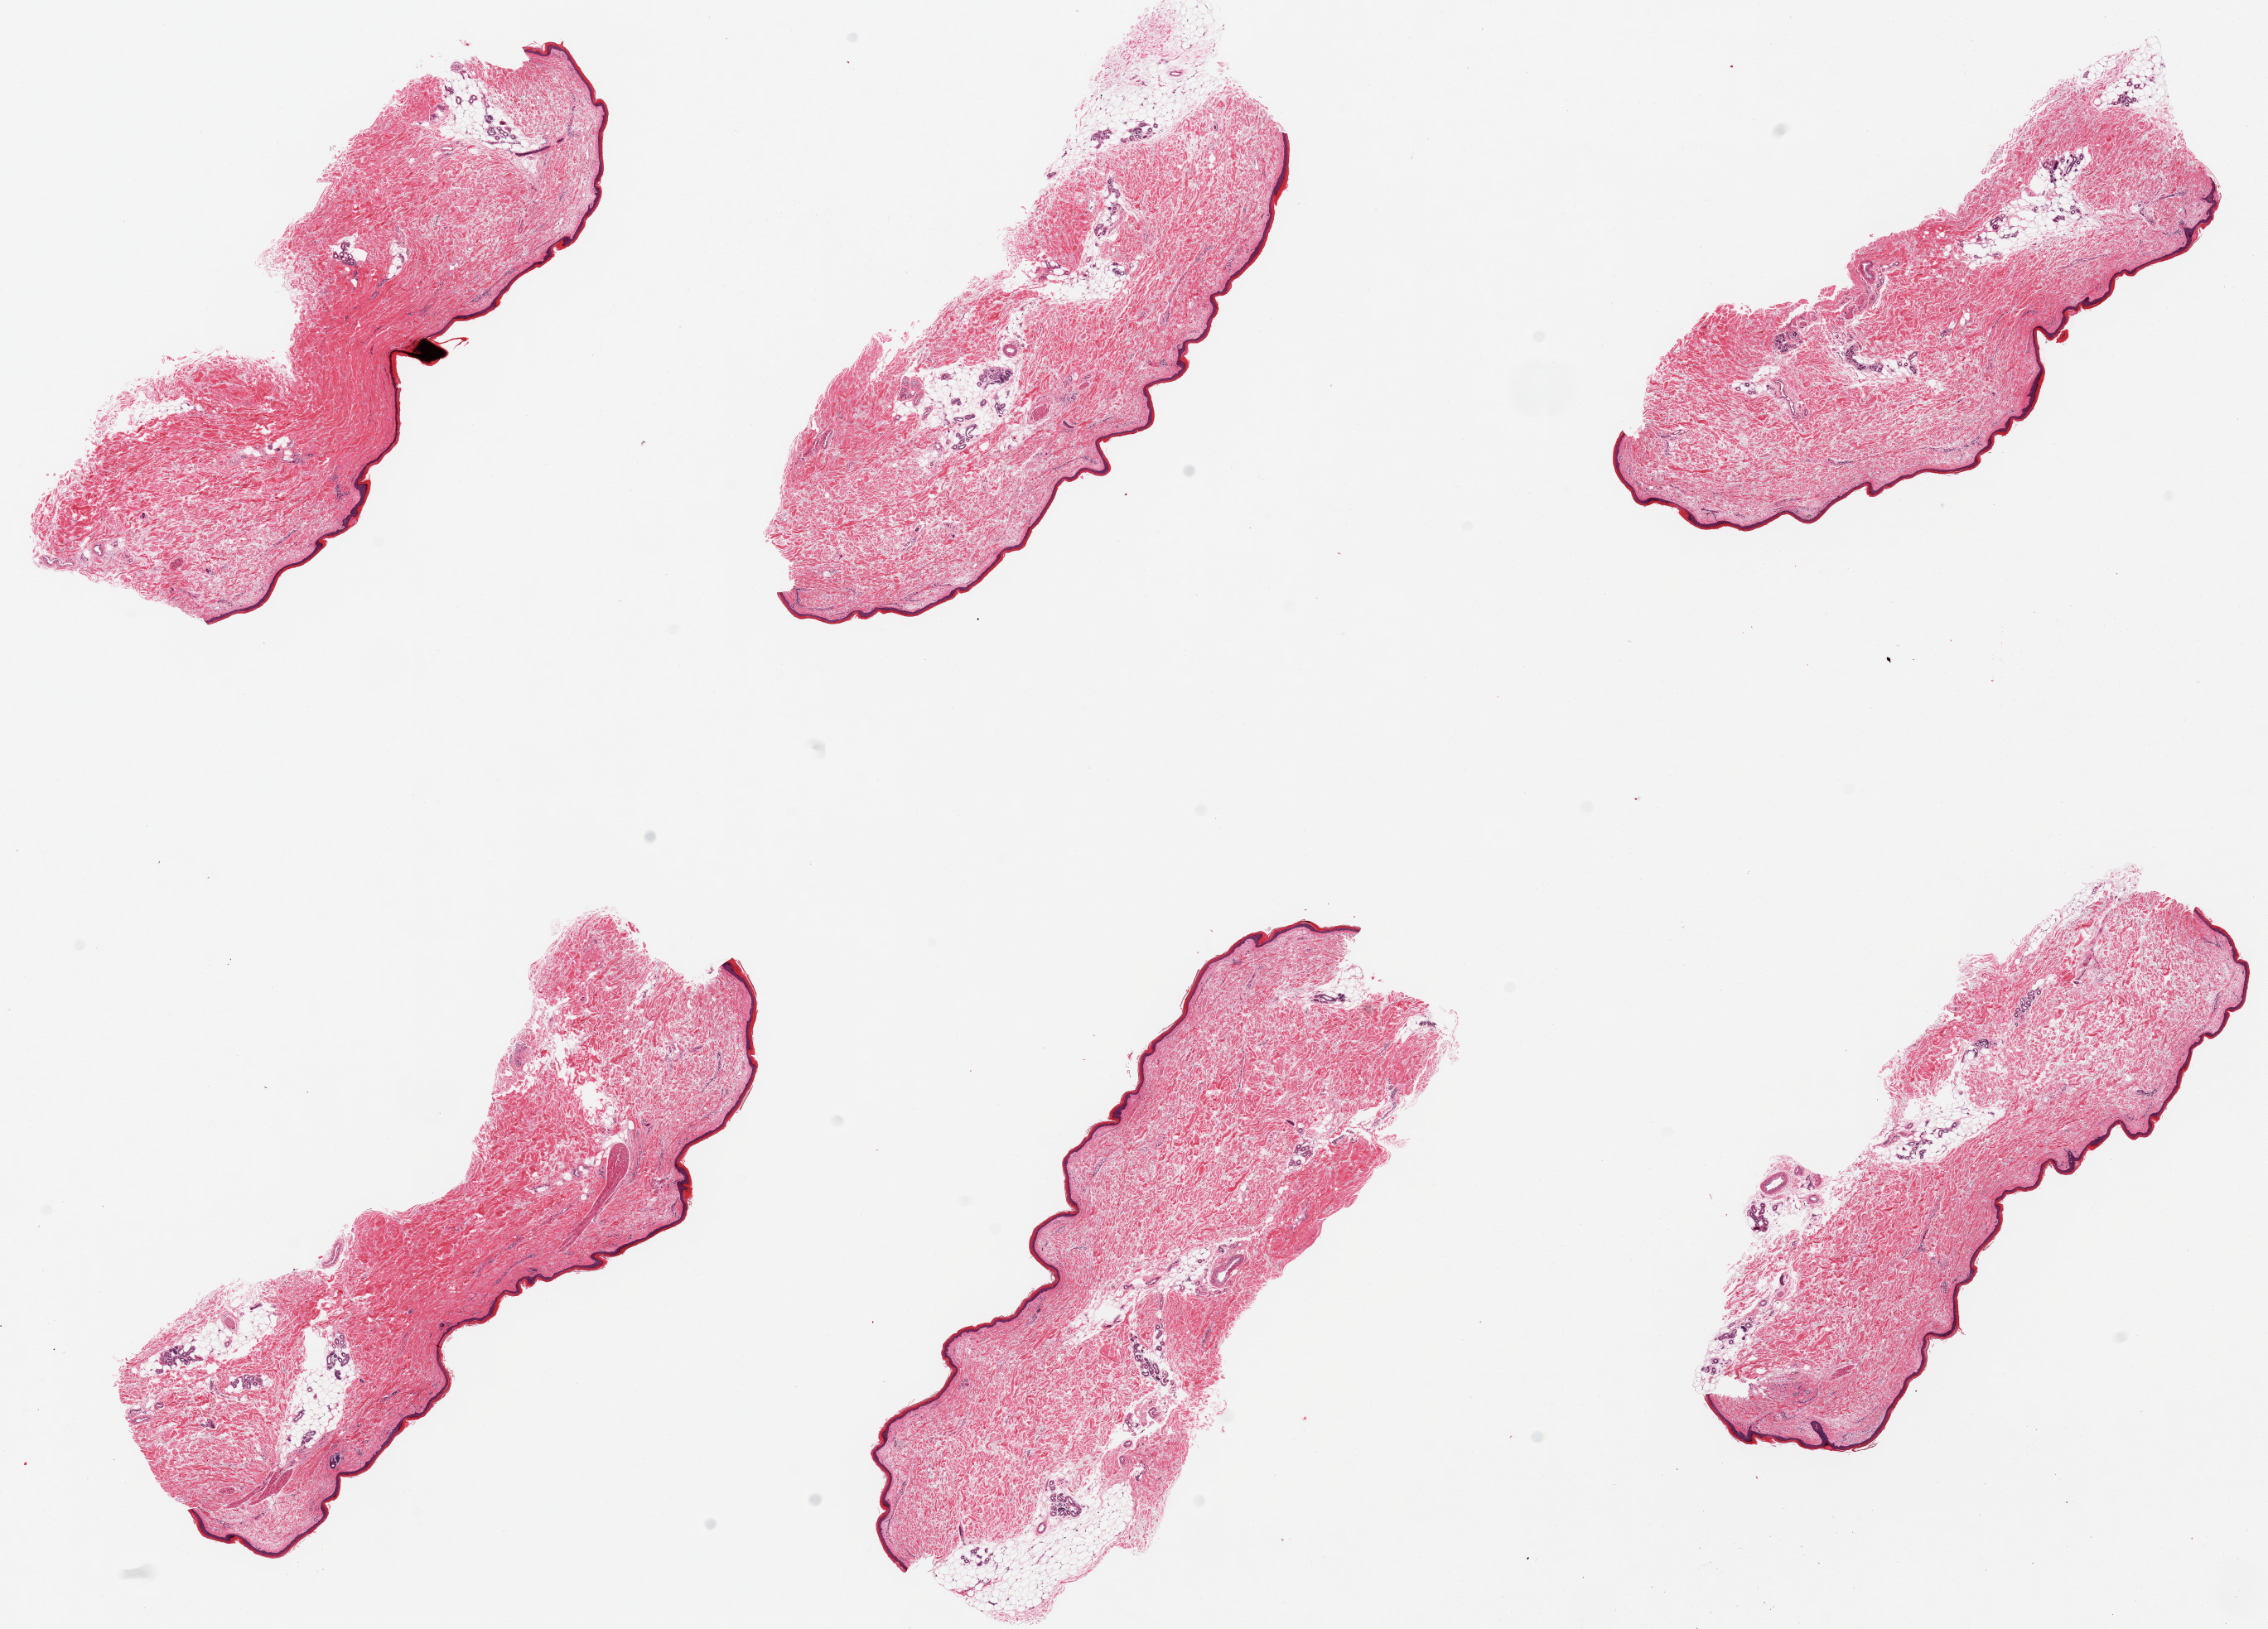
Digitized haematoxylin and eosin-stained section, brightfield, a low-resolution overview of the entire scanned area, about 21.7 x 15.6 mm (from a 20x scan), PAXgene-fixed, paraffin-embedded tissue, section of skin of lower leg (target tissue), donor tissue sample. Donor: male.
• pathologist's review note for this sample: 6 pieces, minimal dermal fat; squamous epithelium is ~30 microns